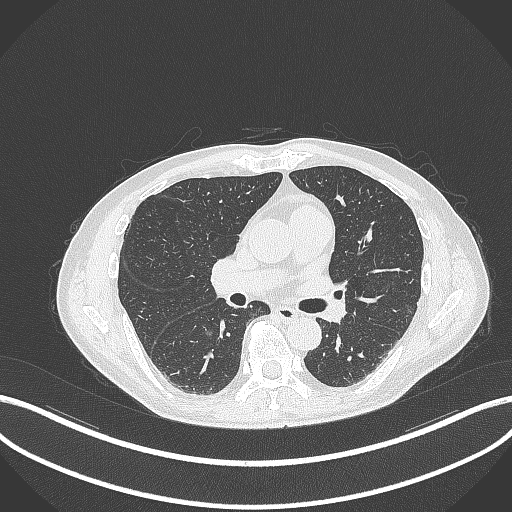
Chest CT, one axial slice; reconstruction kernel B70f; 120 kVp; lung window (W 1500 / L -600 HU); 1 mm slice thickness; 512 × 512 image matrix, field of view 400 × 400 mm. Male patient, age 61 years. From the clinical record (not read from this slice): clinical TNM (as recorded): T1c N0 M0.
Annotated regions visible in this slice (rectangle marked by the reading radiologist):
- lung tumour (recorded histology: adenocarcinoma): bounding box [x1, y1, x2, y2] px = [200, 328, 216, 341]